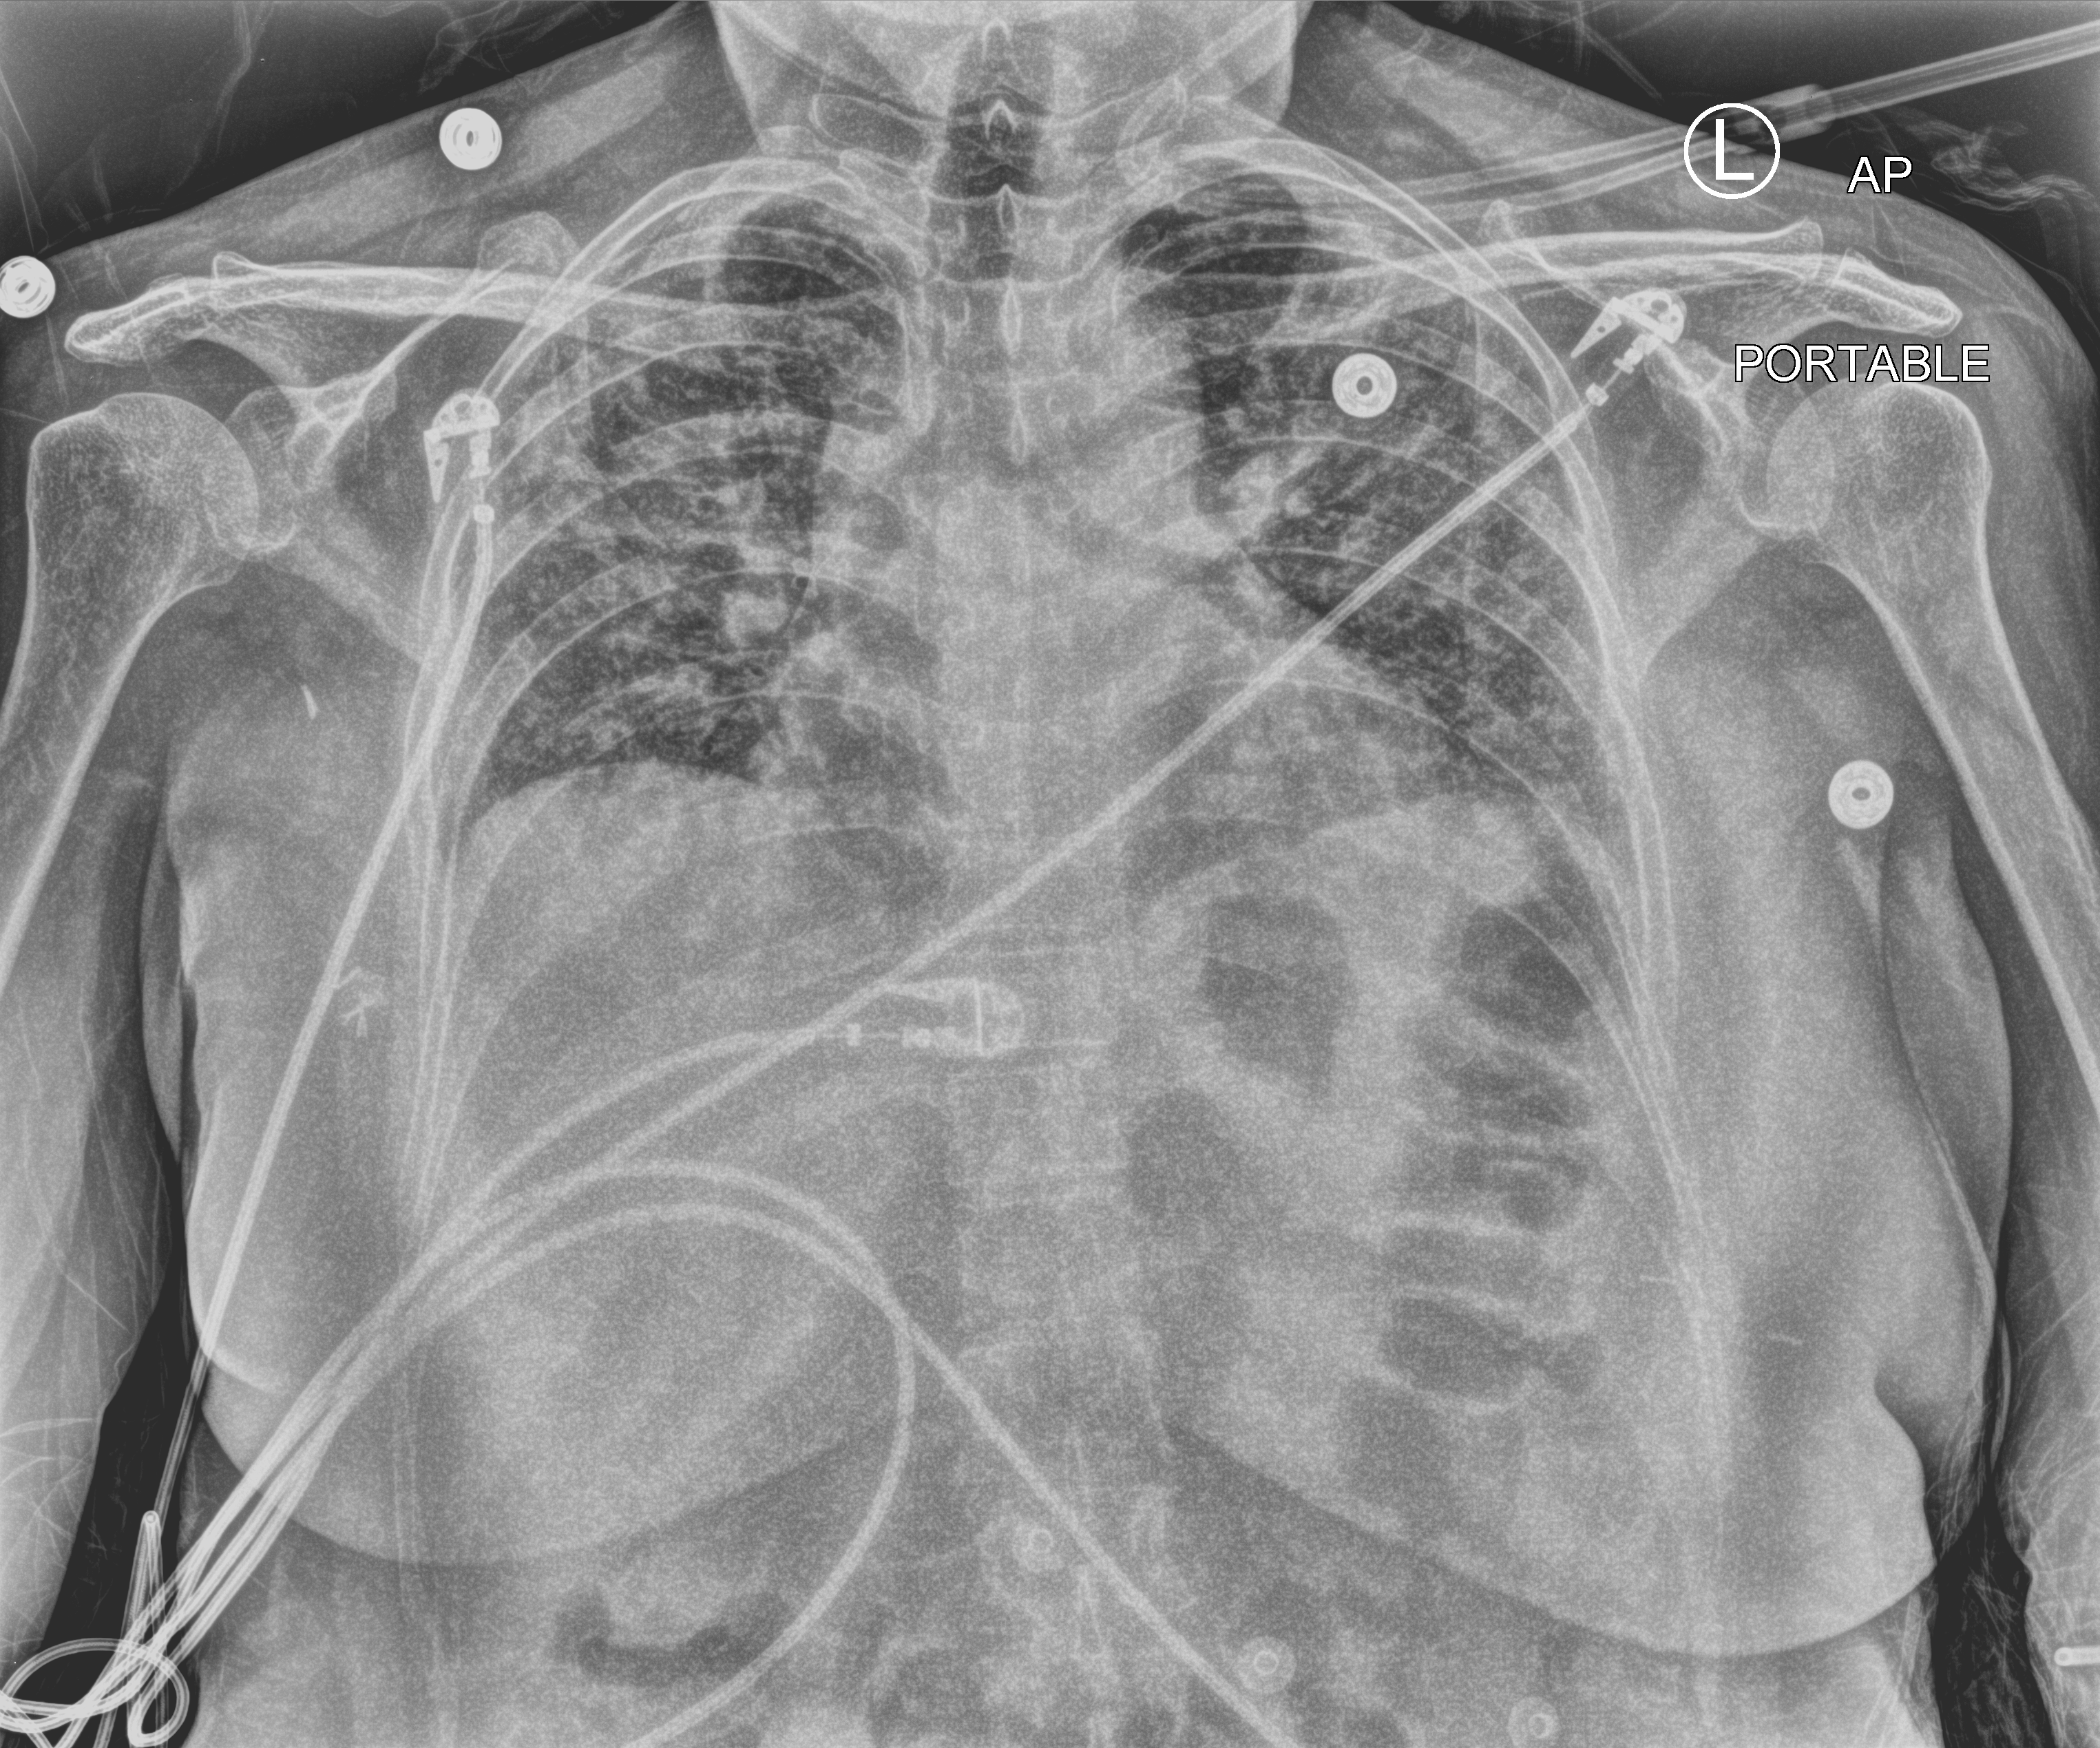
Portable chest radiograph, anteroposterior (AP) projection. Female patient hospitalised with COVID-19, age 18–59 years.
From the hospital-stay record, not from the radiograph (when in the stay this image was taken is not recorded):
- admitted to intensive care during this hospital stay: no